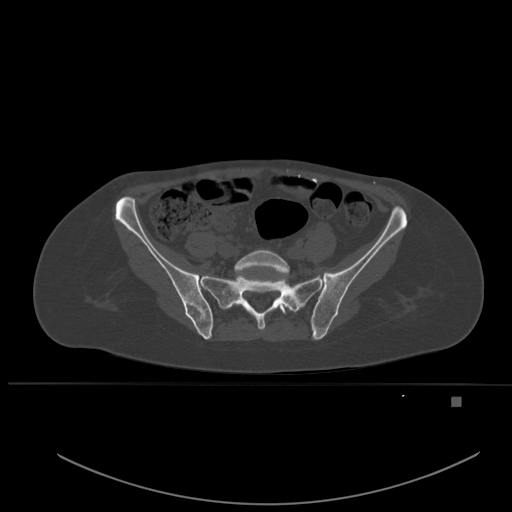
CT including the spine, one axial slice; slice 142 of 651 in the series (ordered by position); bone window (W 1800 / L 400 HU); 1.5 mm slice thickness; 512 × 512 image matrix, field of view 443 × 443 mm. Female patient, age 49 years. Case-level facts recorded for this patient, not image findings: primary cancer: breast; vertebrae with lytic lesions (as recorded): L3, T12, L4.
Annotated regions visible in this slice (semi-automatic segmentation, software-assisted and operator-edited):
- L5 vertebra: bounding box [x1, y1, x2, y2] px = [234, 250, 291, 314]